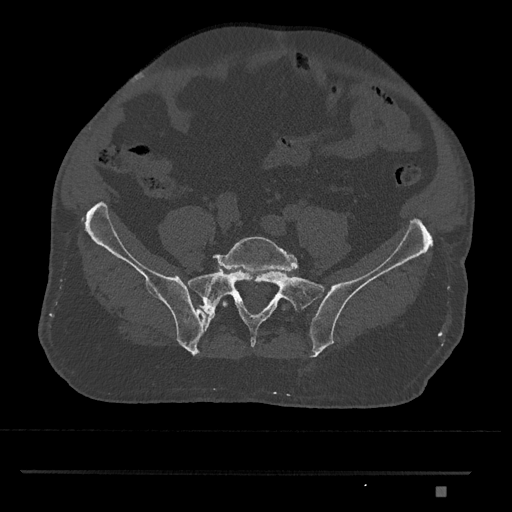
CT including the spine, one axial slice; 120 kVp; bone window (W 1800 / L 400 HU); 0.5 mm slice thickness; 512 × 512 image matrix, field of view 429 × 429 mm. Male patient, age 65 years. Case-level facts recorded for this patient, not image findings: primary cancer: prostate.
Outlined on this slice (semi-automatically segmented with operator editing):
- L5 vertebra: bounding box (x1, y1, x2, y2) in pixels: (213, 236, 299, 308)